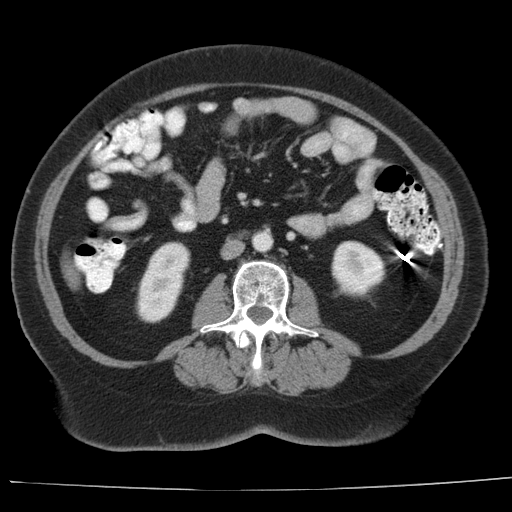
Contrast-enhanced abdominal CT, one axial slice; slice 1 of 44 in the series (ordered by position); reconstruction kernel AA-1; 140 kVp; intravenous contrast given; soft-tissue window (W 400 / L 40 HU); 5 mm slice thickness; 512 × 512 image matrix, field of view 373 × 373 mm. Female patient. From the clinical record (not read from this slice): diagnosis: colorectal cancer liver metastases, imaged before liver resection; multiple liver metastases: yes; largest metastasis: 1.8 cm; disease in both lobes: no.
Outlined on this slice (outlined manually by an expert reader):
- liver: bounding box (x1, y1, x2, y2) in pixels: (60, 249, 79, 289)